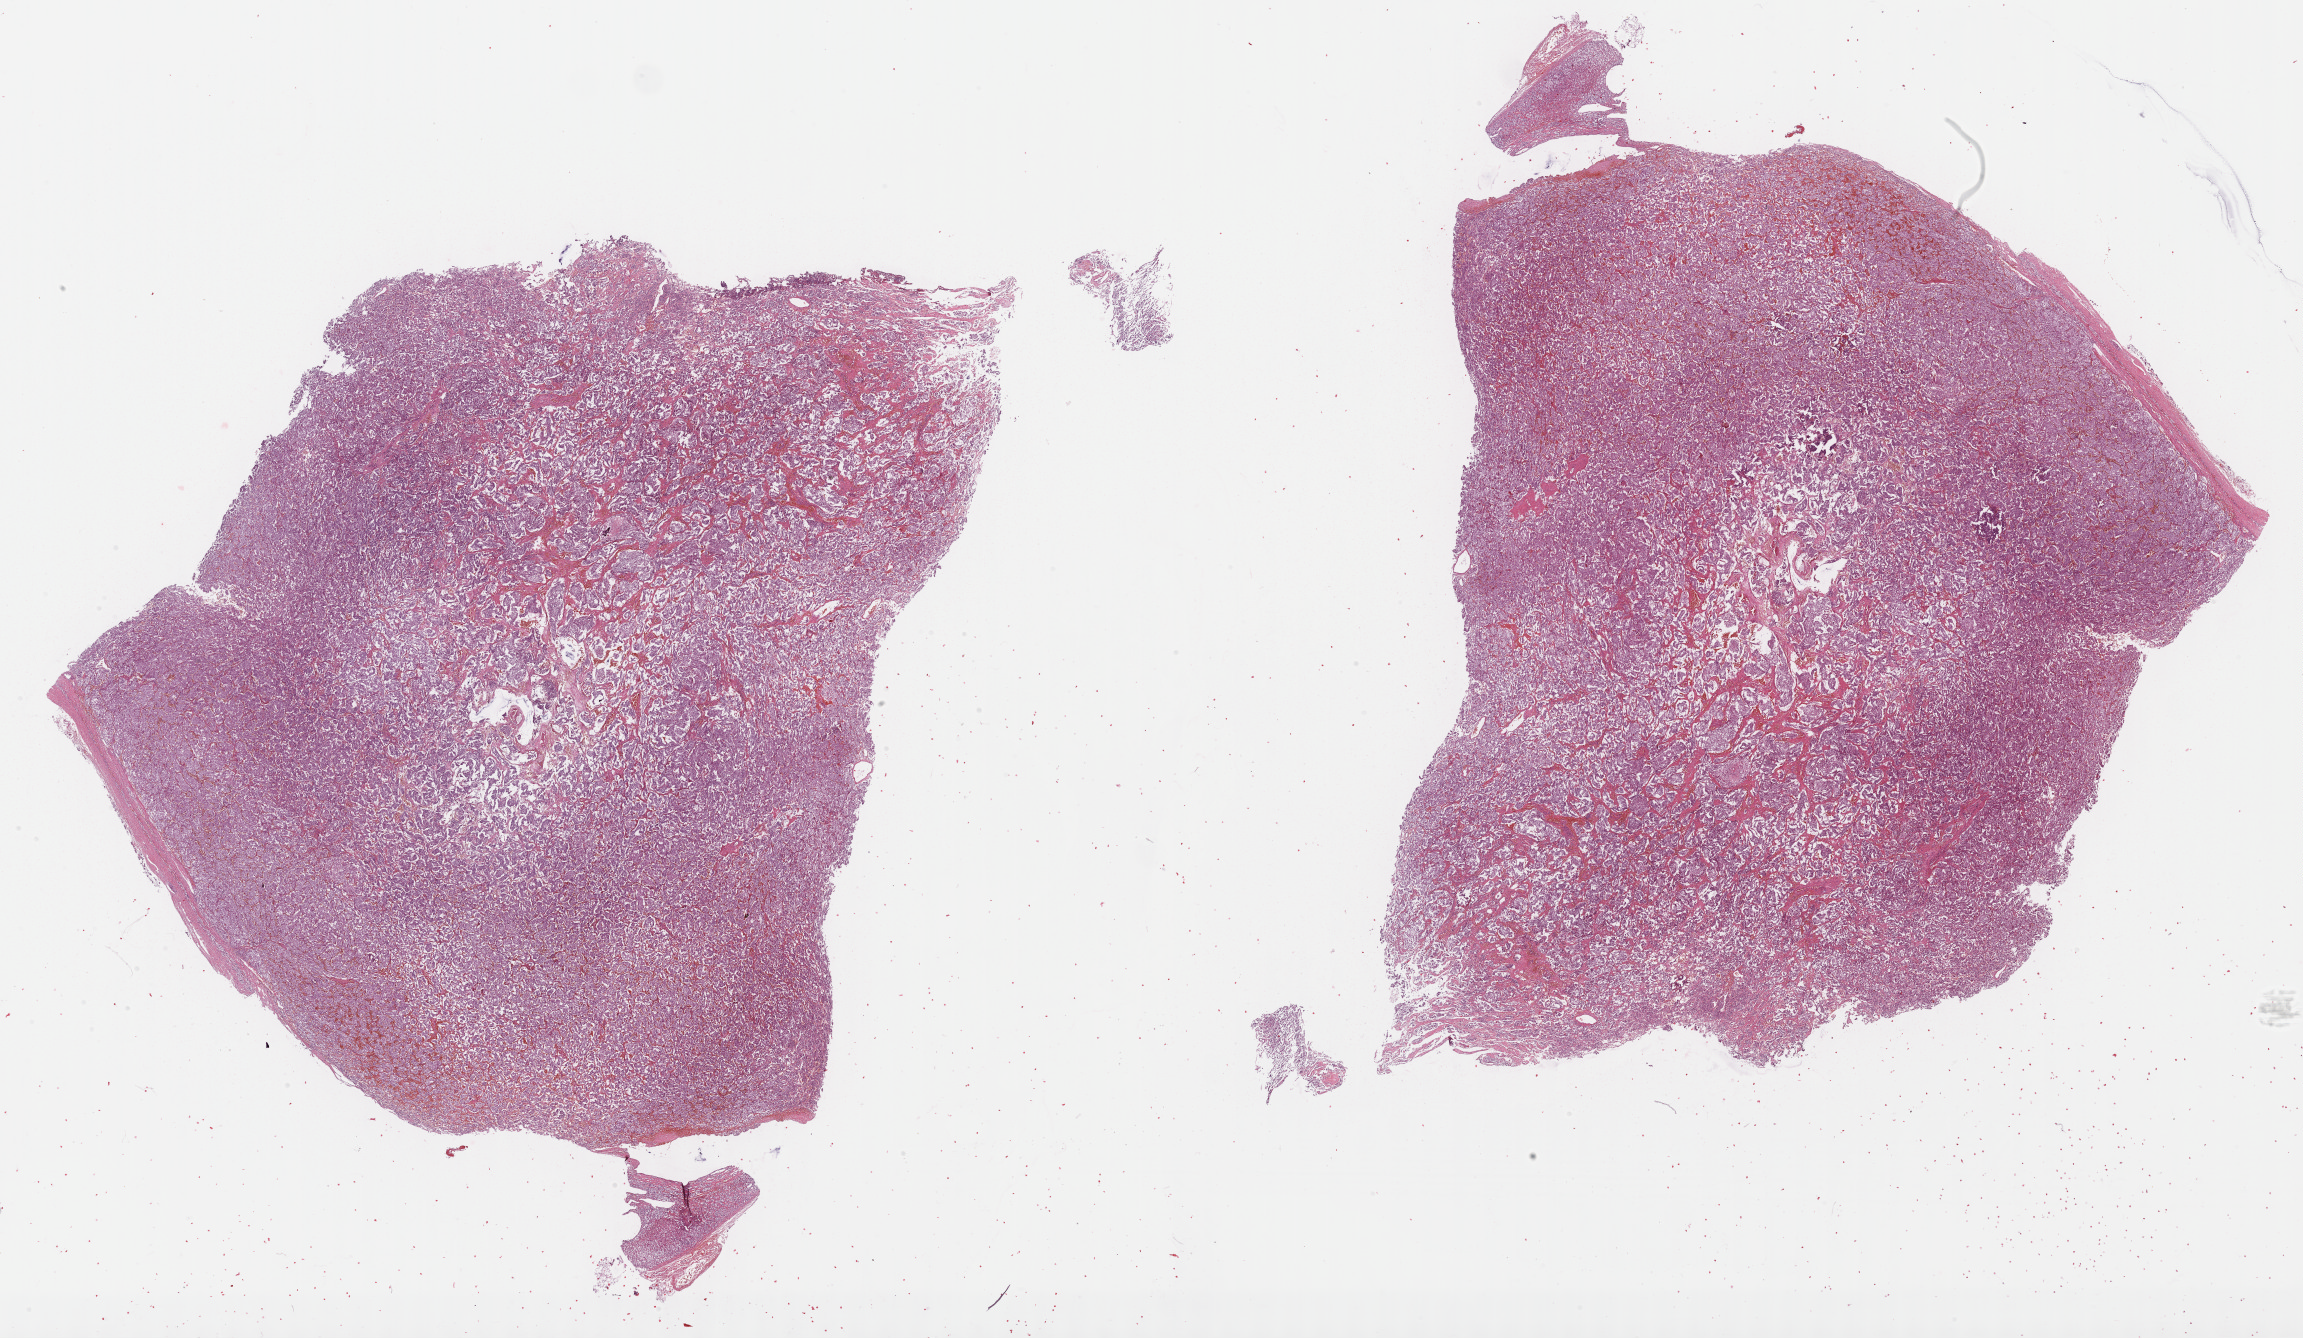
Whole-slide histology image, H&E, whole scanned area (about 37.2 x 21.6 mm, from a 40x scan) shown as a low-resolution overview. Formalin-fixed paraffin-embedded (FFPE) diagnostic section. Primary tumour sample from the adrenal gland. Patient: female, age at initial diagnosis 32 years.
Histologic diagnosis: Pheochromocytoma, NOS.